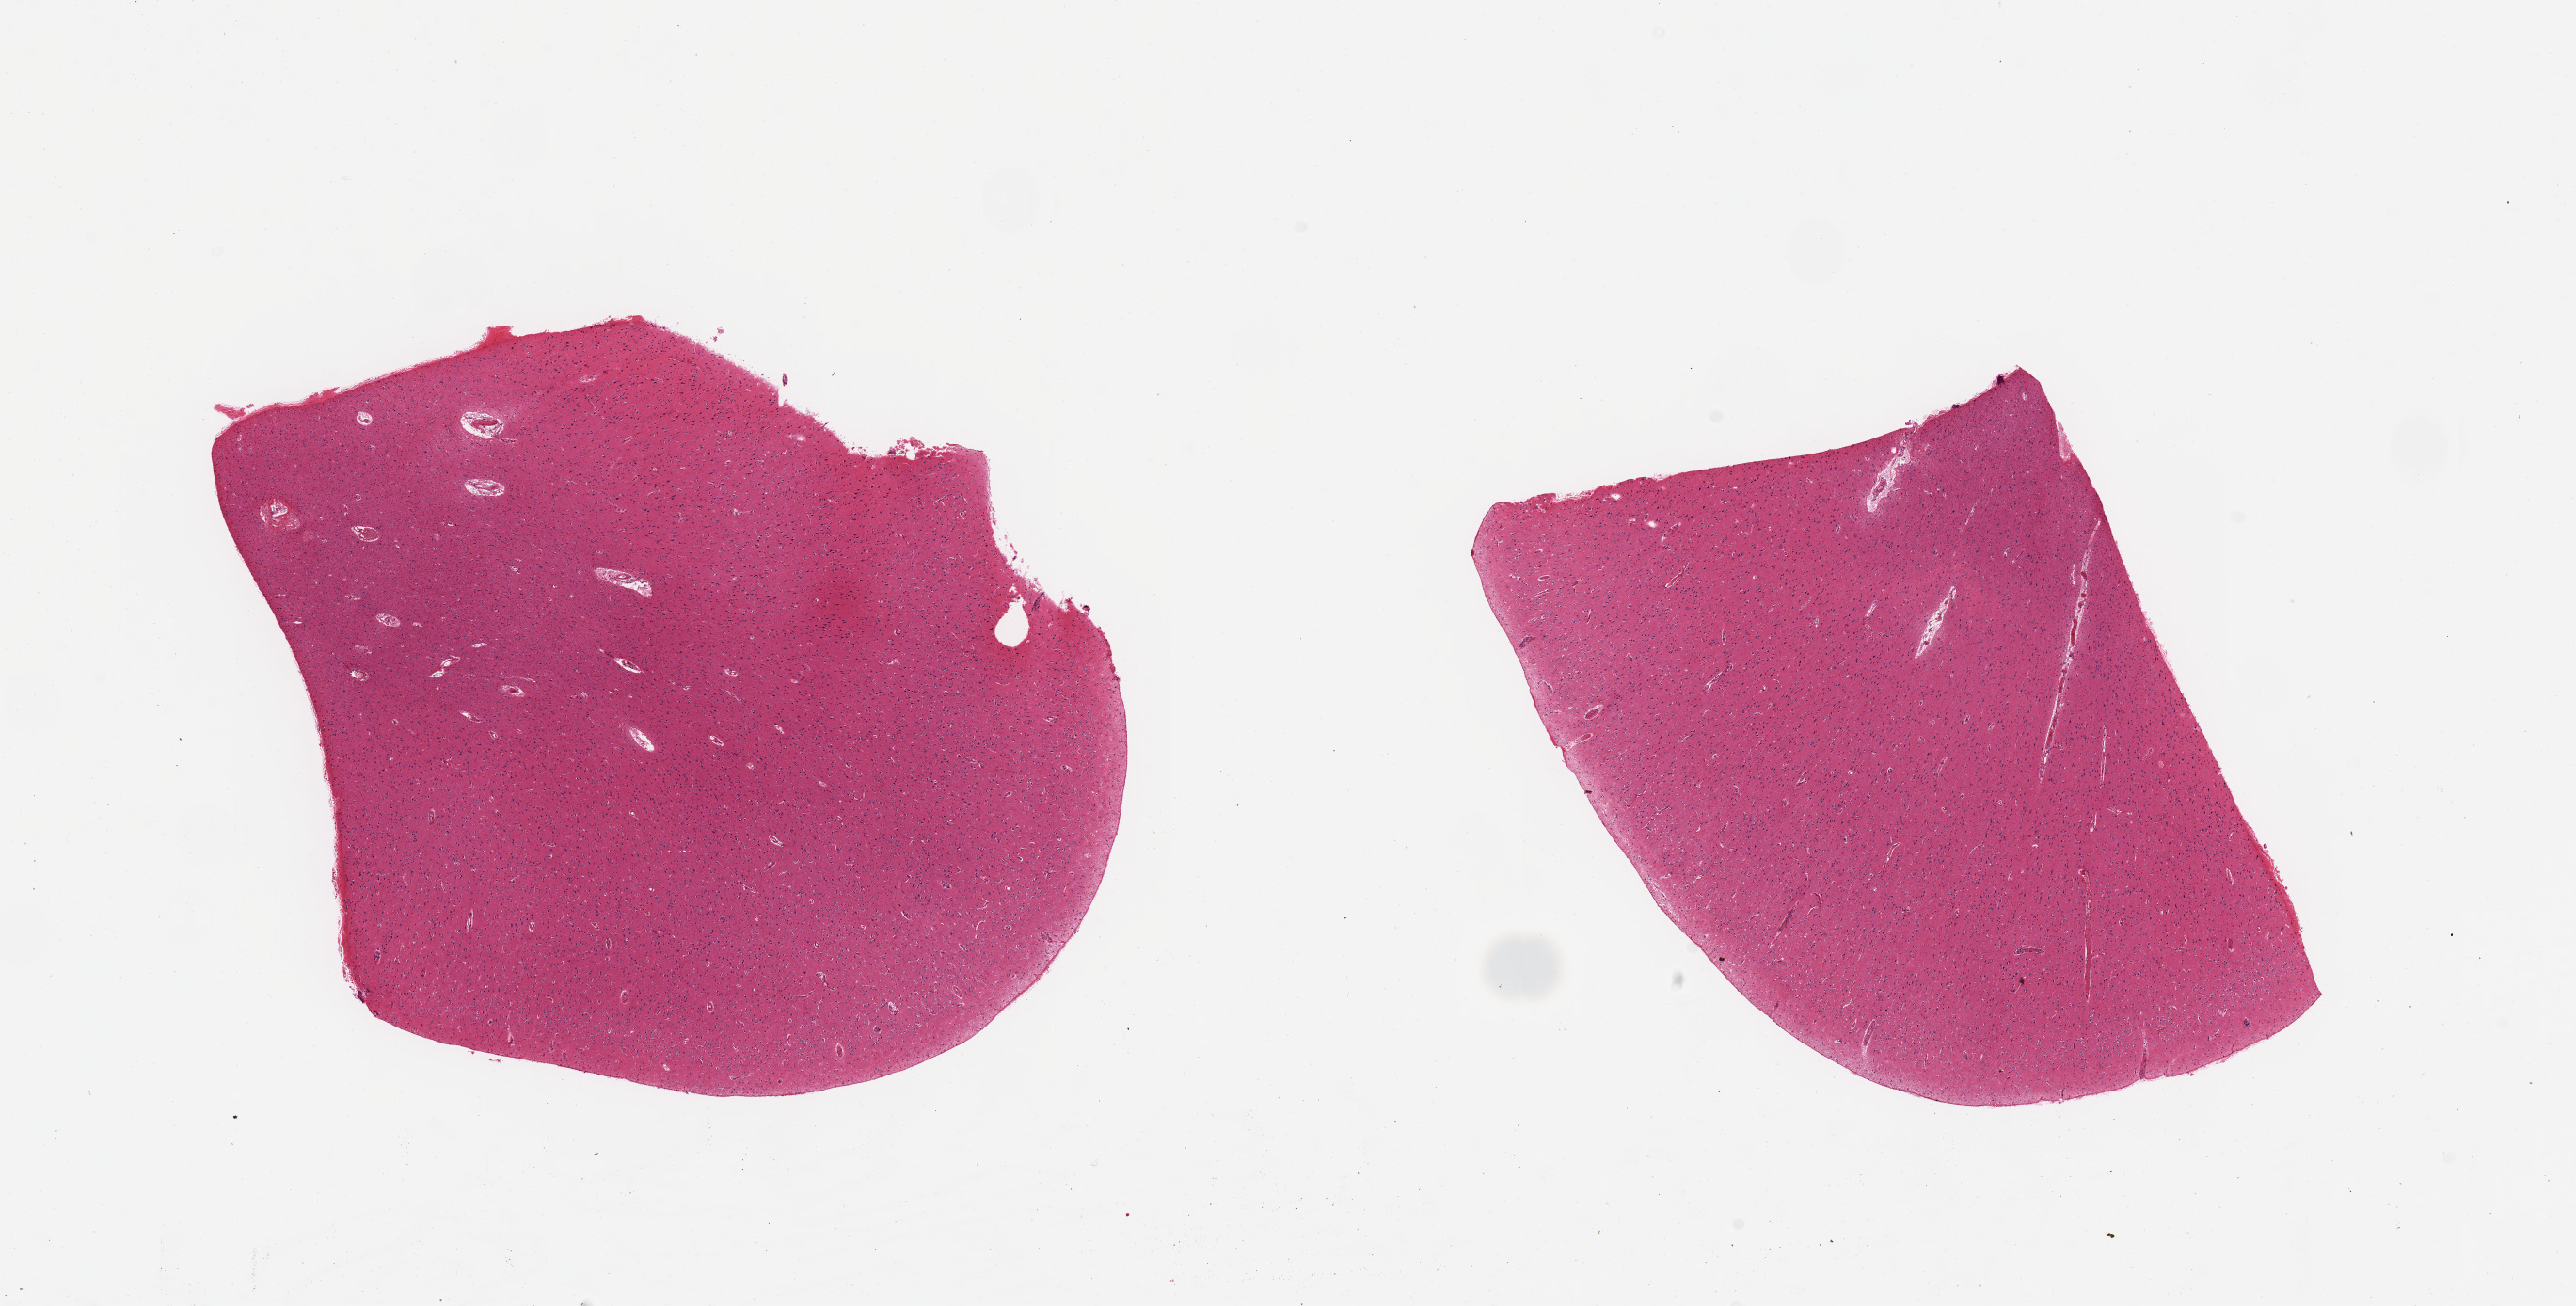
Digitized haematoxylin and eosin-stained section, a low-resolution overview of the entire scanned area, about 21.7 x 11.0 mm (from a 20x scan), PAXgene-fixed paraffin-embedded (PFPE) section, sampled site (target tissue): cerebral cortex, donor tissue sample. Donor: male.
* review note (as recorded): Well-preserved